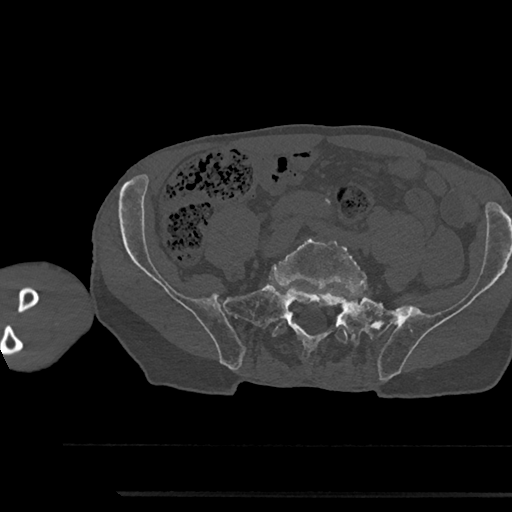
CT including the spine, one axial slice; position 315 of 797 along the scan axis; reconstruction kernel Br40s/3; 120 kVp; bone window (W 1800 / L 400 HU); 0.5 mm slice thickness; 512 × 512 image matrix, field of view 367 × 367 mm. Patient: male, 79 years. Case-level facts recorded for this patient, not image findings: primary cancer: prostate.
Annotated regions visible in this slice (semi-automatically segmented with operator editing):
- L5 vertebra: bounding box [x1, y1, x2, y2] px = [272, 235, 367, 343]